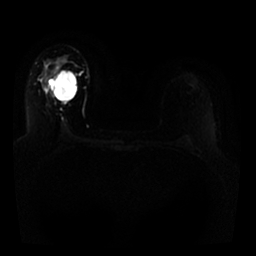
Breast MRI, one axial slice; position 18 of 25 along the scan axis; diffusion-weighted series; image 2 of 4 stored at this slice position (different b-values; order by instance number); 1.5 T; 256 × 256 image matrix. Female patient.
Annotated regions visible in this slice (expert manual segmentation):
- tumour on diffusion-weighted imaging: box from (x=49, y=71) to (x=60, y=96) px